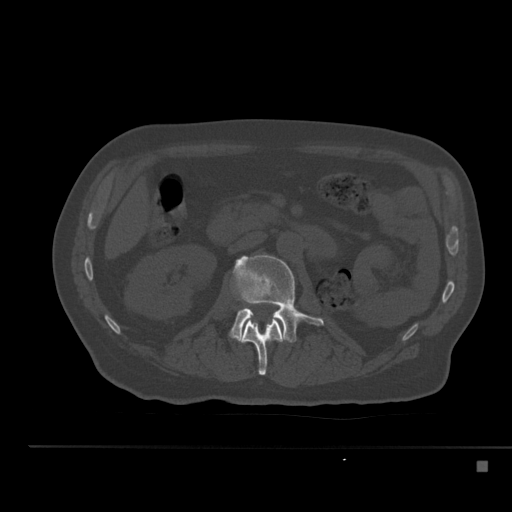
CT including the spine, one axial slice; 120 kVp; bone window (W 1800 / L 400 HU); 512 × 512 image matrix, field of view 408 × 408 mm. Patient: male, 70 years. Case-level facts recorded for this patient, not image findings: primary cancer: renal.
Structures marked on this image (semi-automatic segmentation, software-assisted and operator-edited):
- L1 vertebra: bounding box [x1, y1, x2, y2] px = [238, 318, 286, 376]
- L2 vertebra: [230, 254, 324, 343]